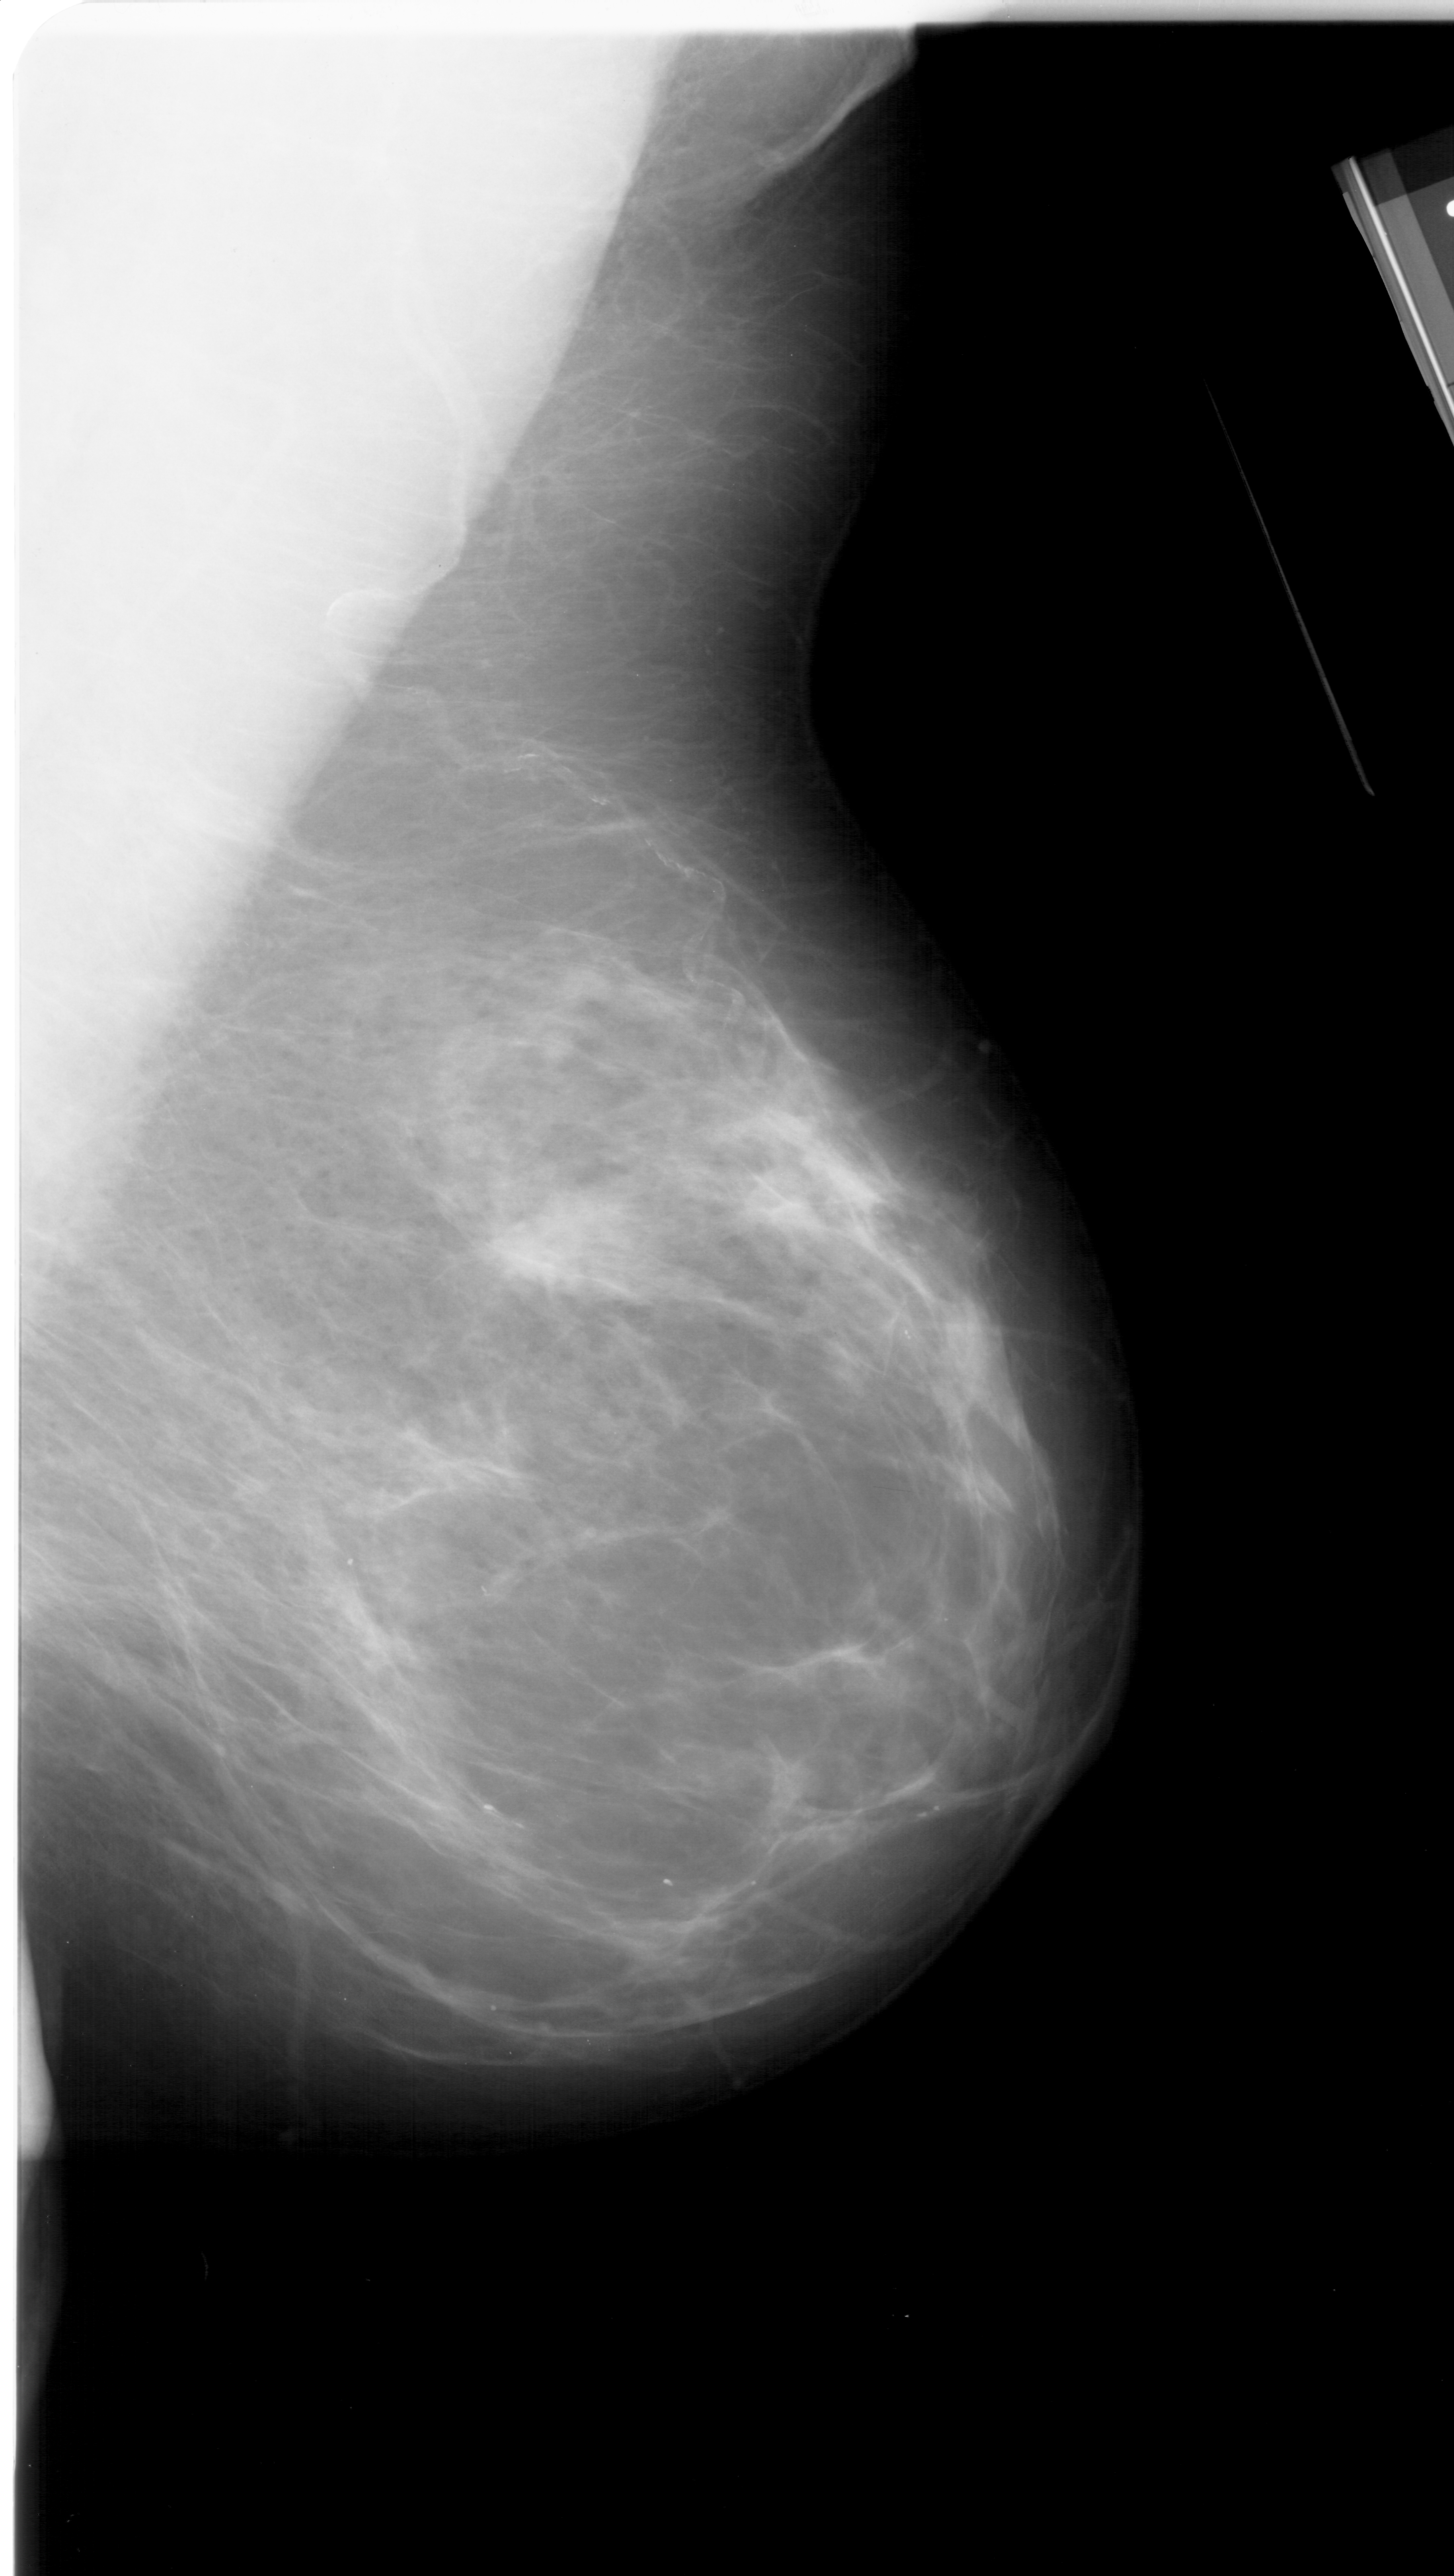
Mammogram (digitized film), right breast, MLO view.
Radiologist-marked abnormalities on this image: mass, shape irregular, margins spiculated; BI-RADS assessment category 4; pathology result (as recorded, not read from the image): malignant.